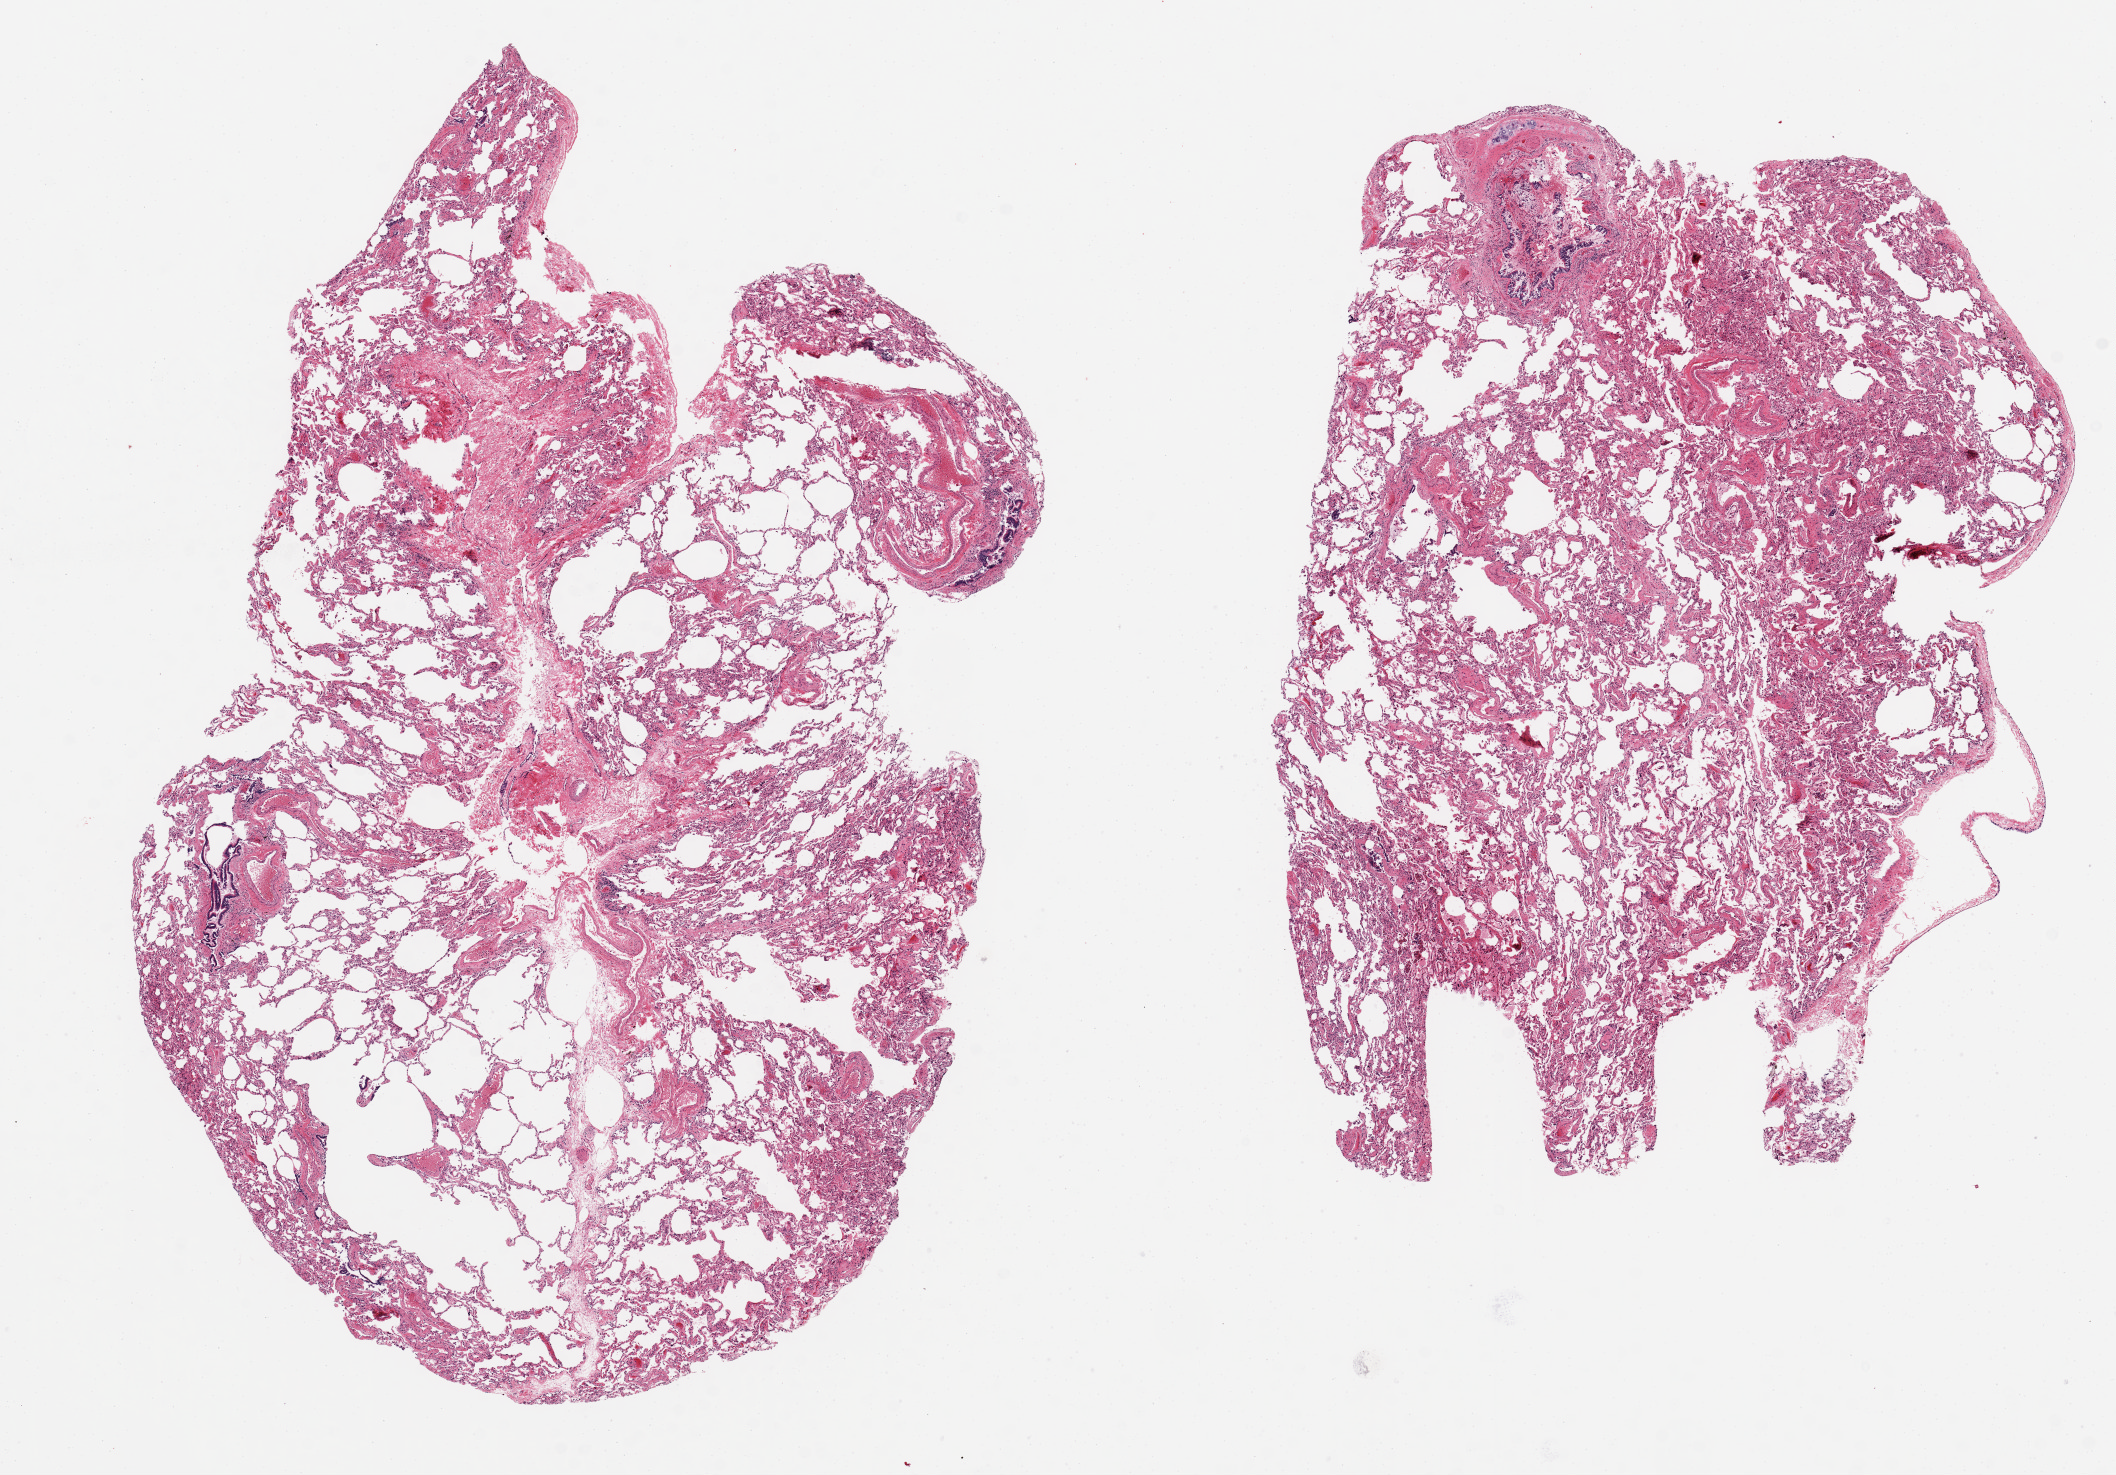
Whole-slide image, haematoxylin and eosin stain, low-resolution overview of the scanned area, about 16.7 x 11.7 mm (from a 20x scan); PAXgene-fixed paraffin-embedded (PFPE) section; target tissue: lung; donor tissue sample. Donor sex: male.
Review note (as recorded): pieces ; patchy alveolar dilatation; focal bronchial hemorrhage.